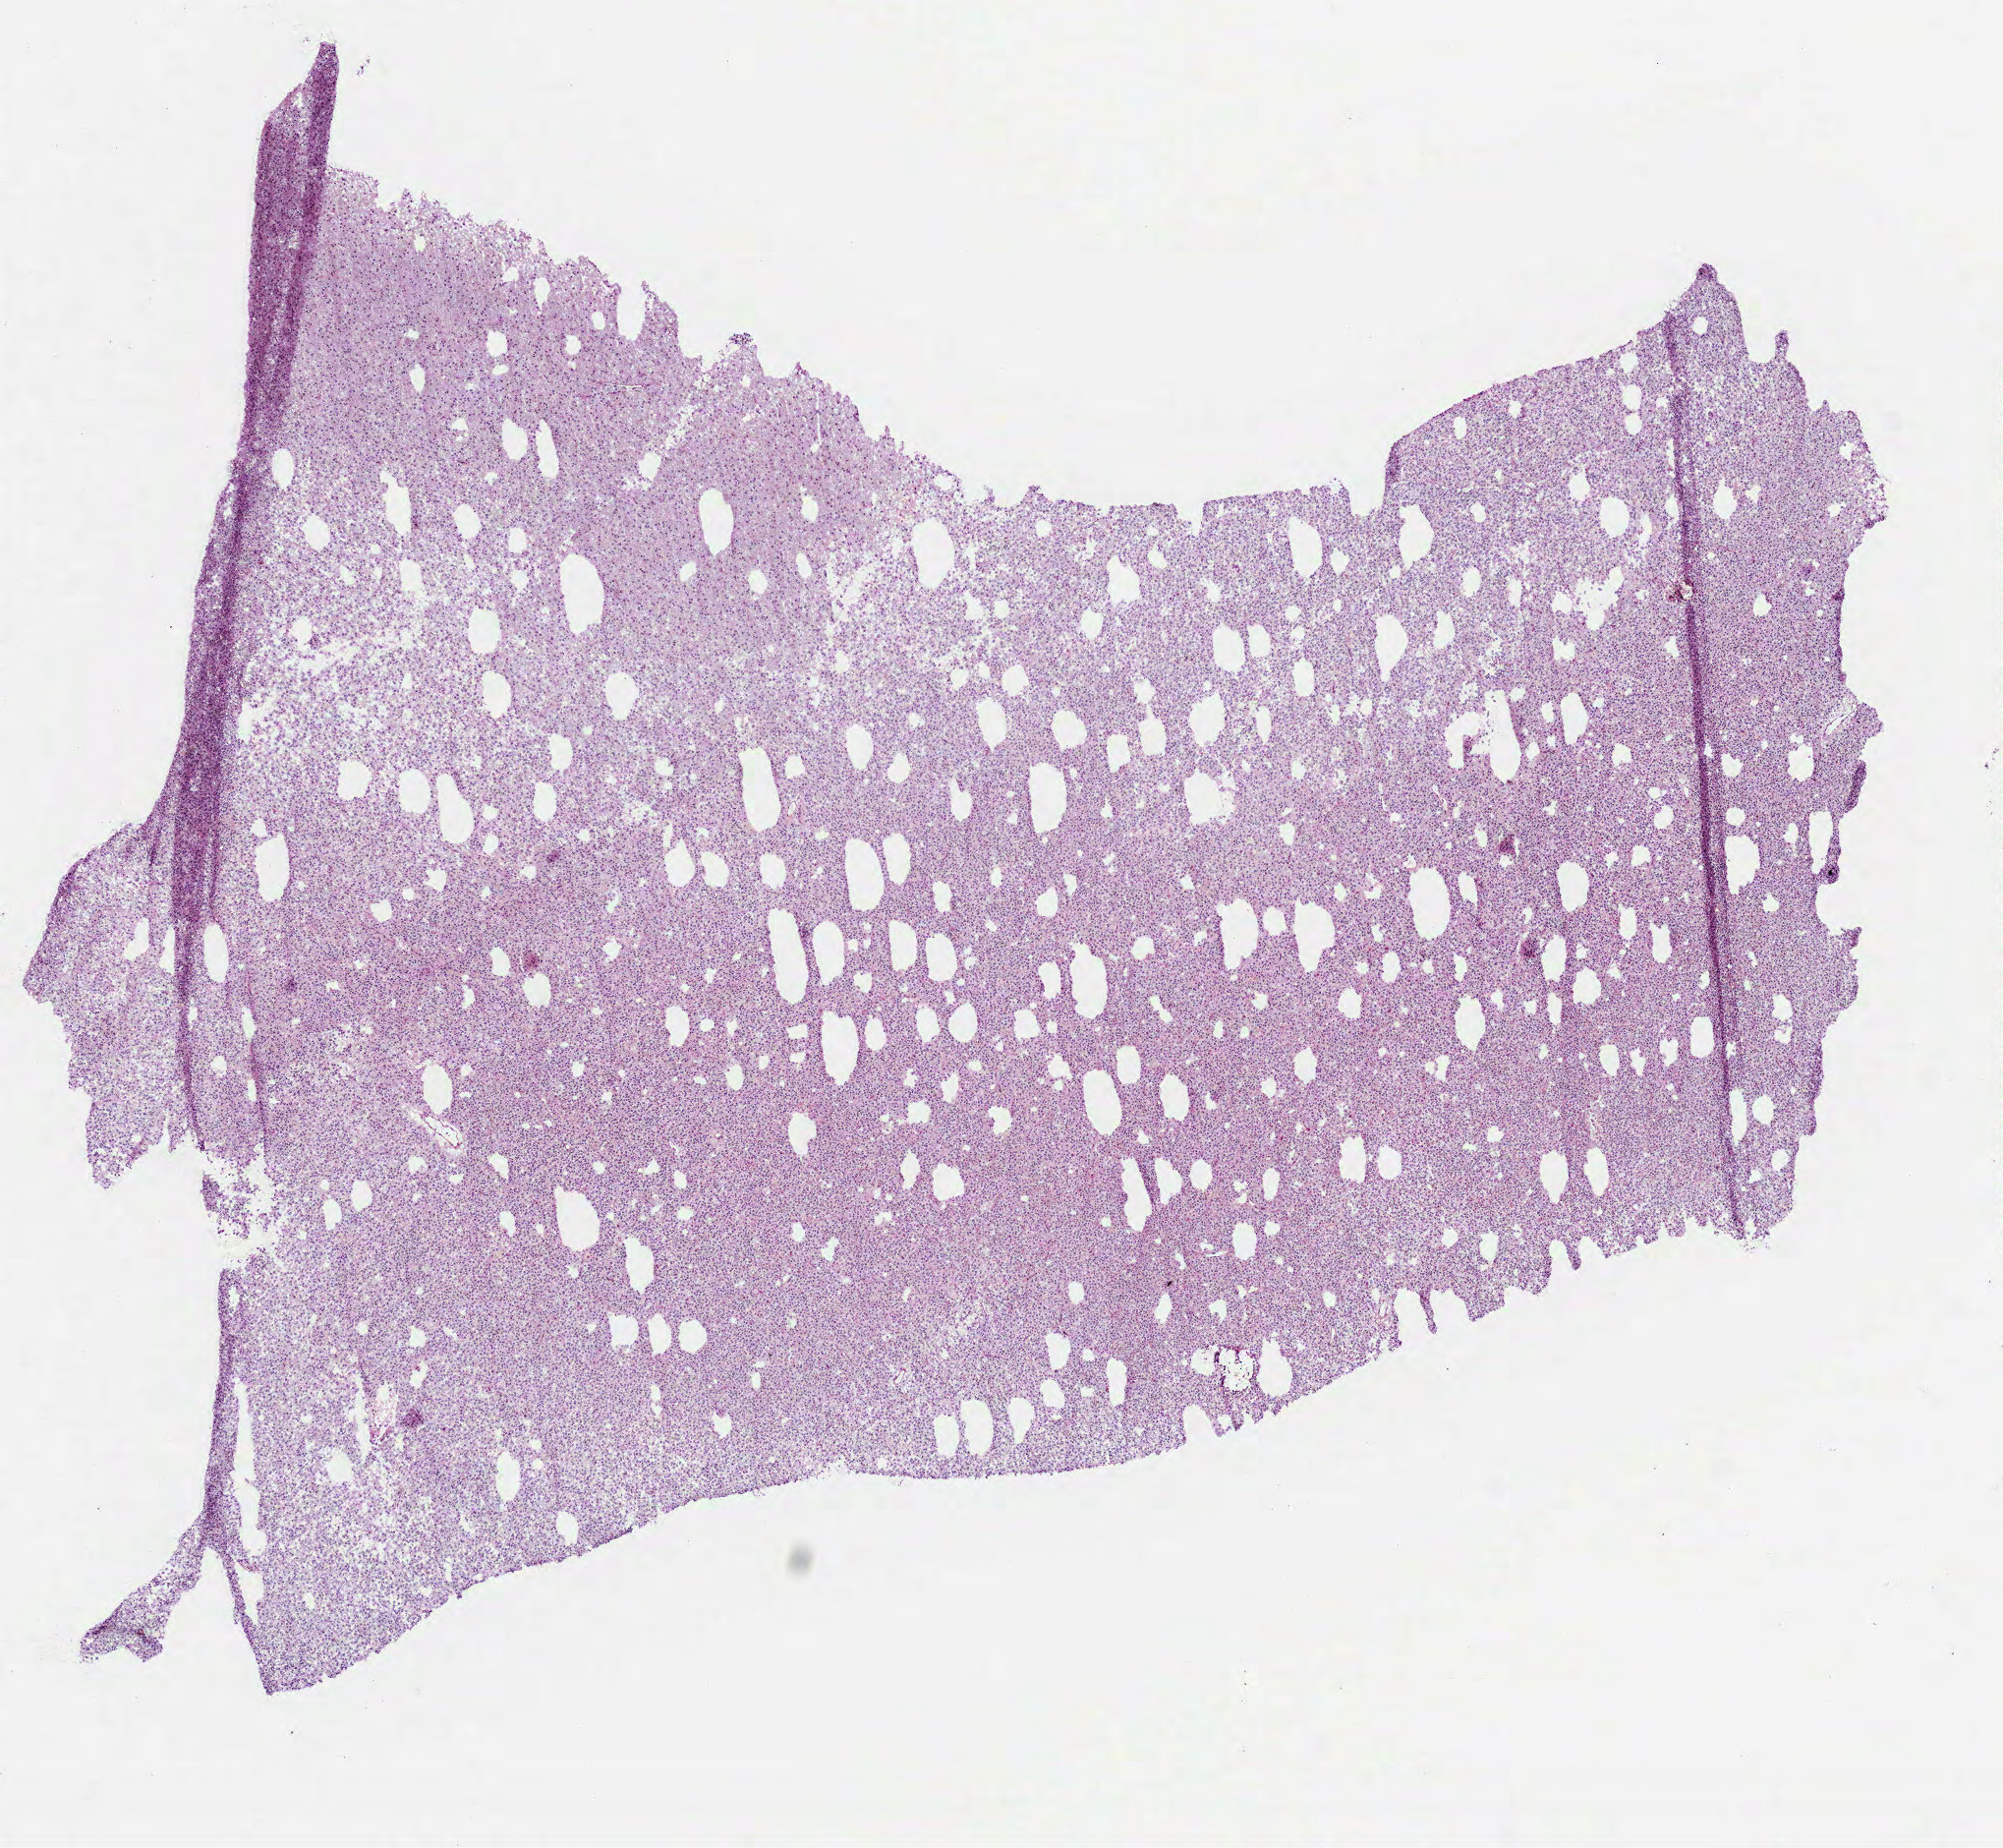
Hematoxylin and eosin (H&E) stained whole-slide image, low-resolution overview of the scanned area, about 8.2 x 7.6 mm (slide scanned at 40x); frozen section; primary tumour sample from the brain. Patient: female, age at initial diagnosis 47 years. Histologic grade: G2 (moderately differentiated). Slide review estimates, as recorded: tumour cells 100%, tumour nuclei 85%, normal cells 0%, stromal cells 0%, necrosis 0%.
- diagnosis: Oligodendroglioma, NOS